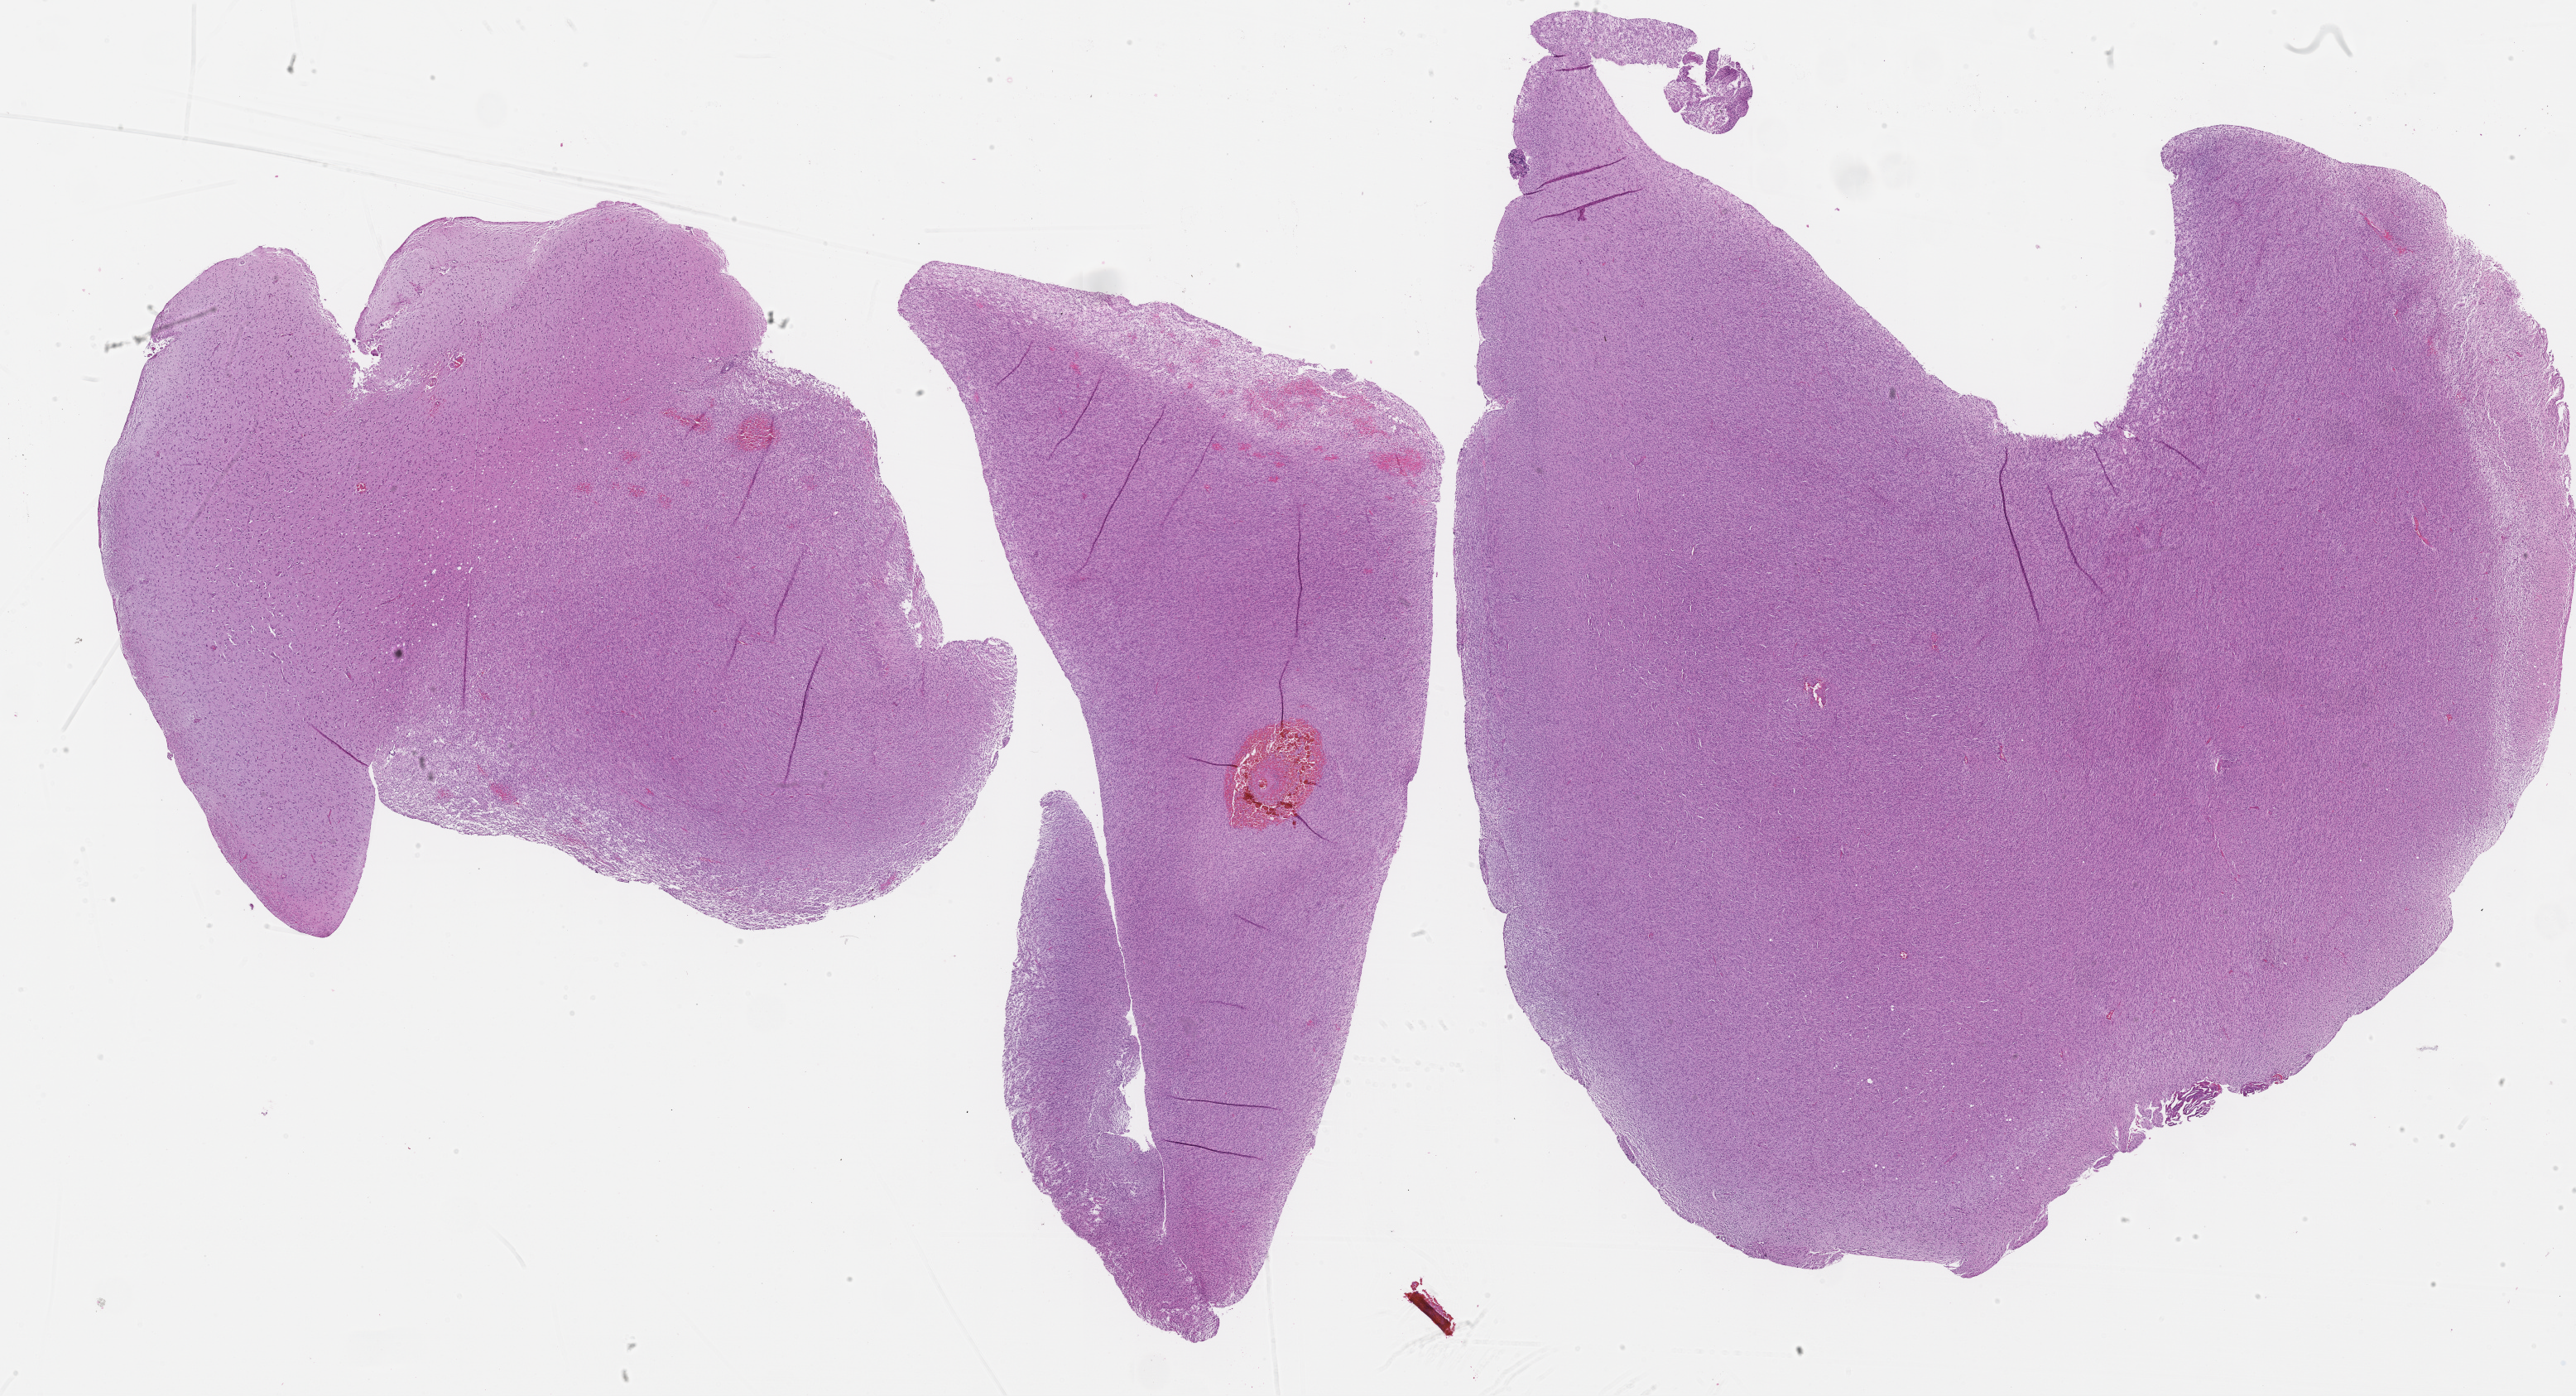
Digitized Hematoxylin and eosin (H&E) stained tissue section (whole slide), low-resolution overview of the scanned area, about 25.2 x 13.7 mm (slide scanned at 40x). Formalin-fixed paraffin-embedded (FFPE) diagnostic section. Brain, primary tumour sample. Patient: female, age at initial diagnosis 61 years.
Pathologic diagnosis: Glioblastoma.